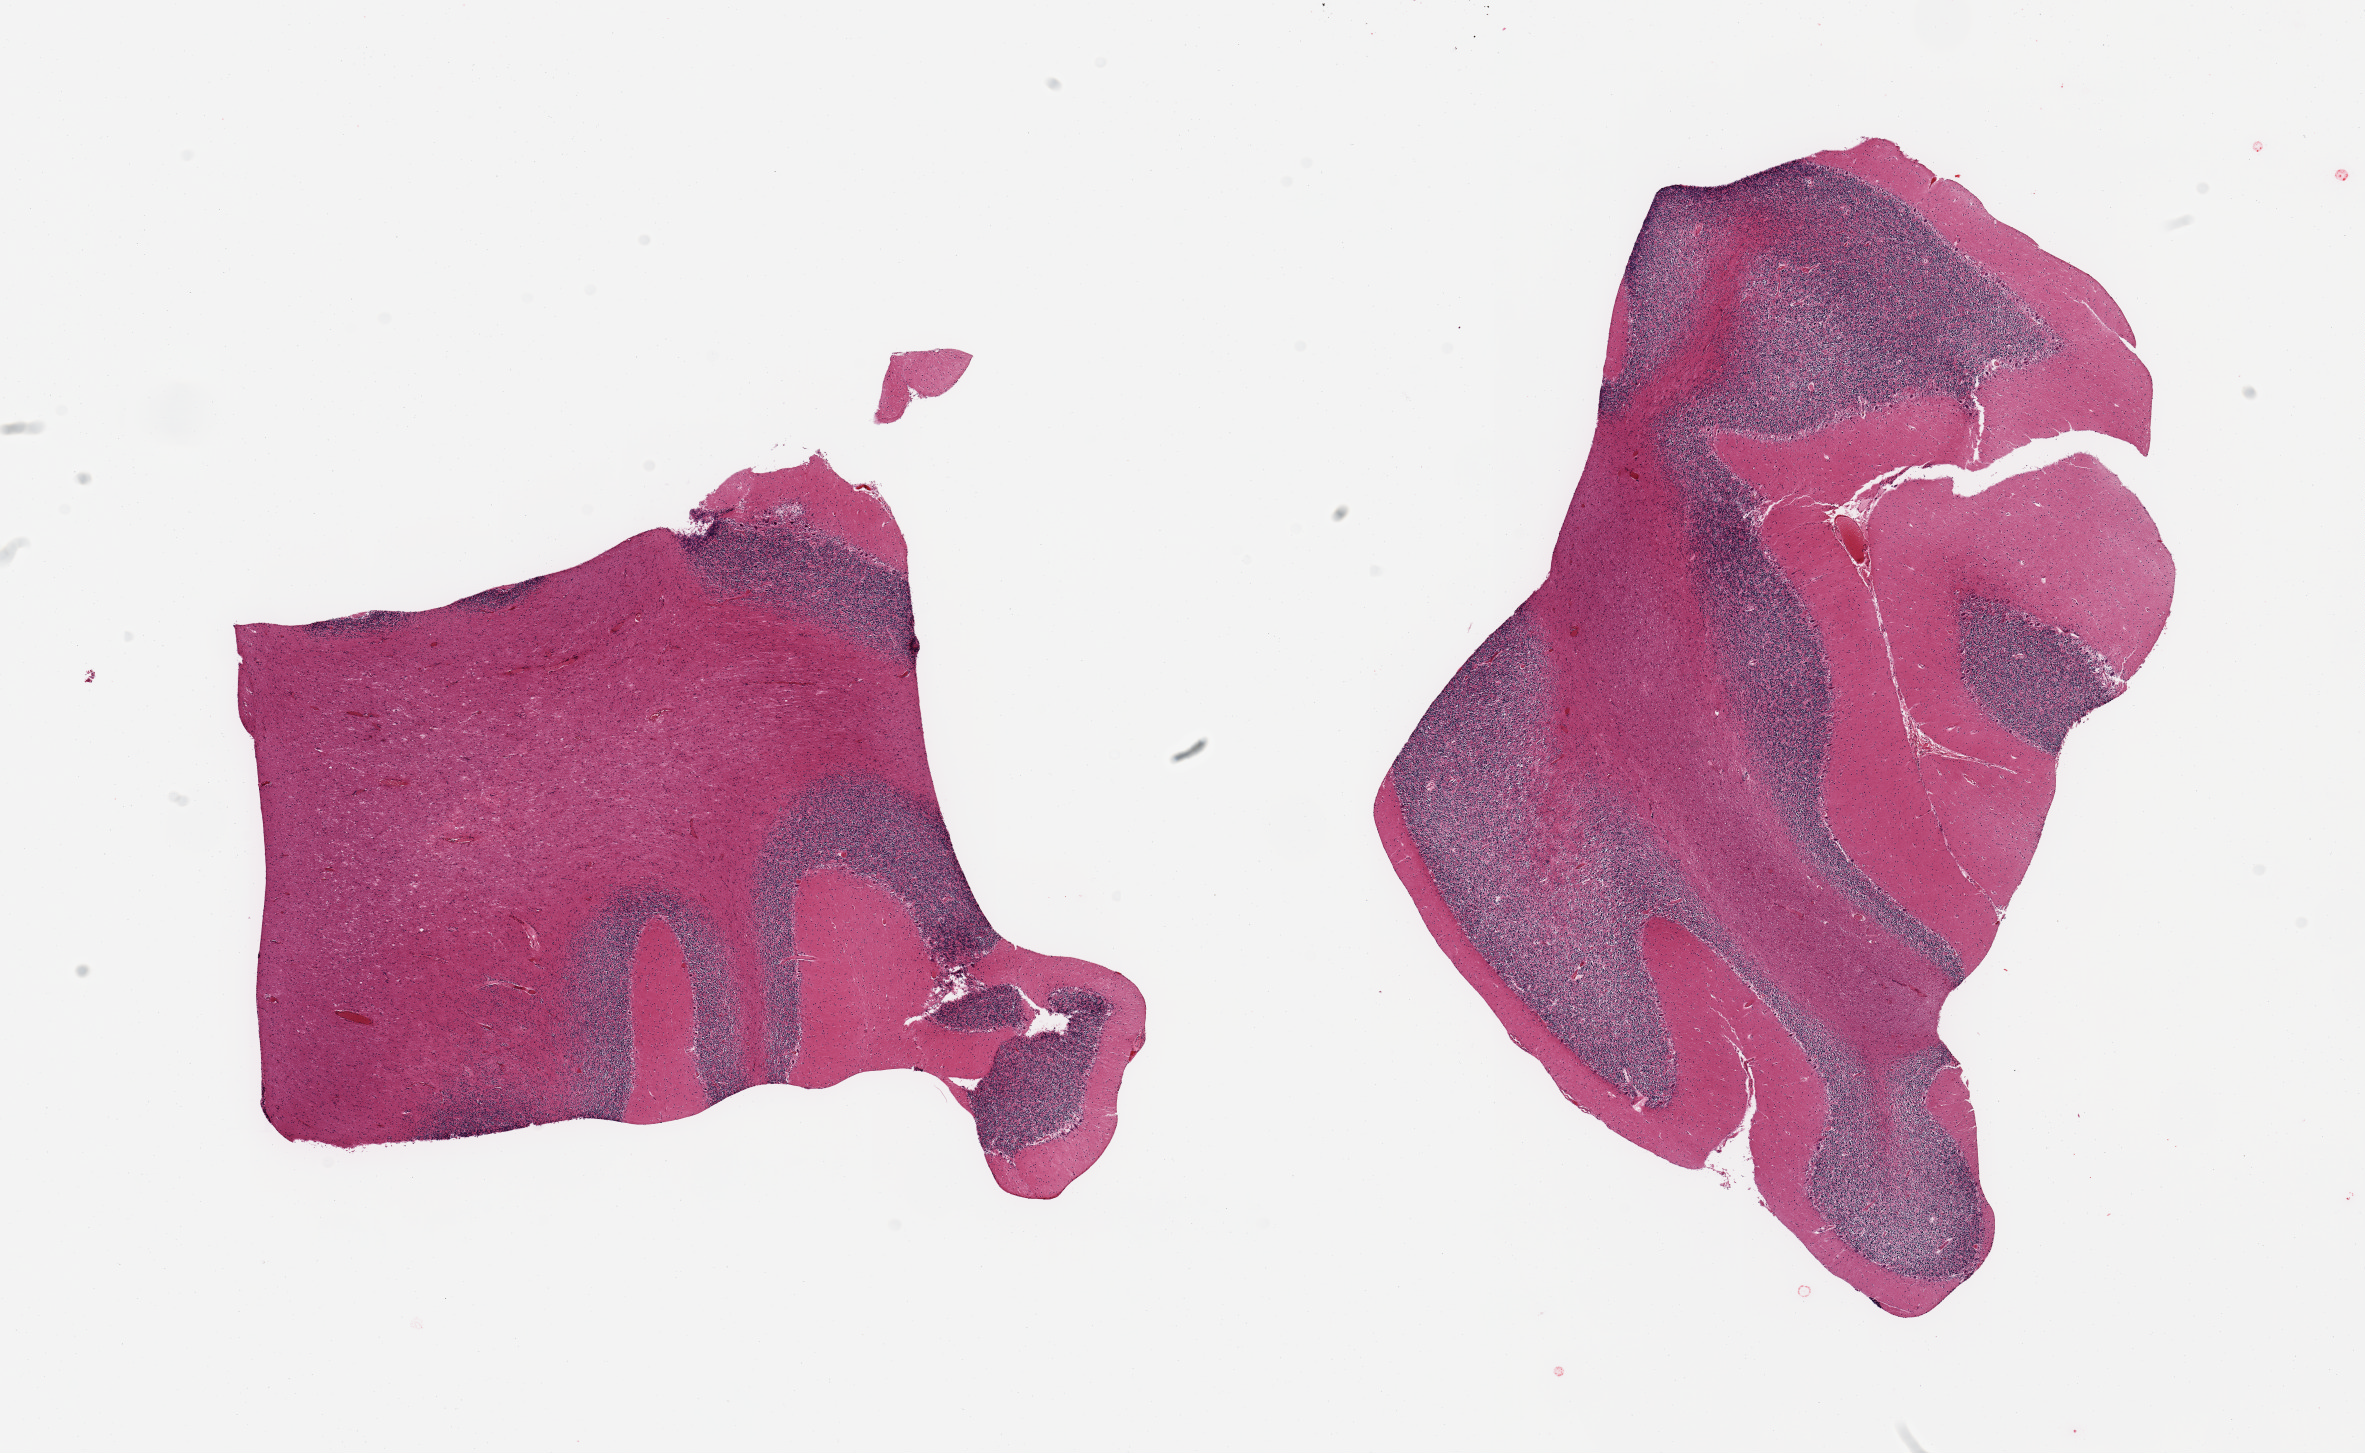
Hematoxylin and eosin (H&E) whole-slide image, whole scanned area (about 18.7 x 11.5 mm) shown as a low-resolution overview; PAXgene-fixed paraffin-embedded (PFPE) section; target tissue: cerebellum; tissue donor sample. Male donor.
Pathologist's review note for this sample: 2 pieces.